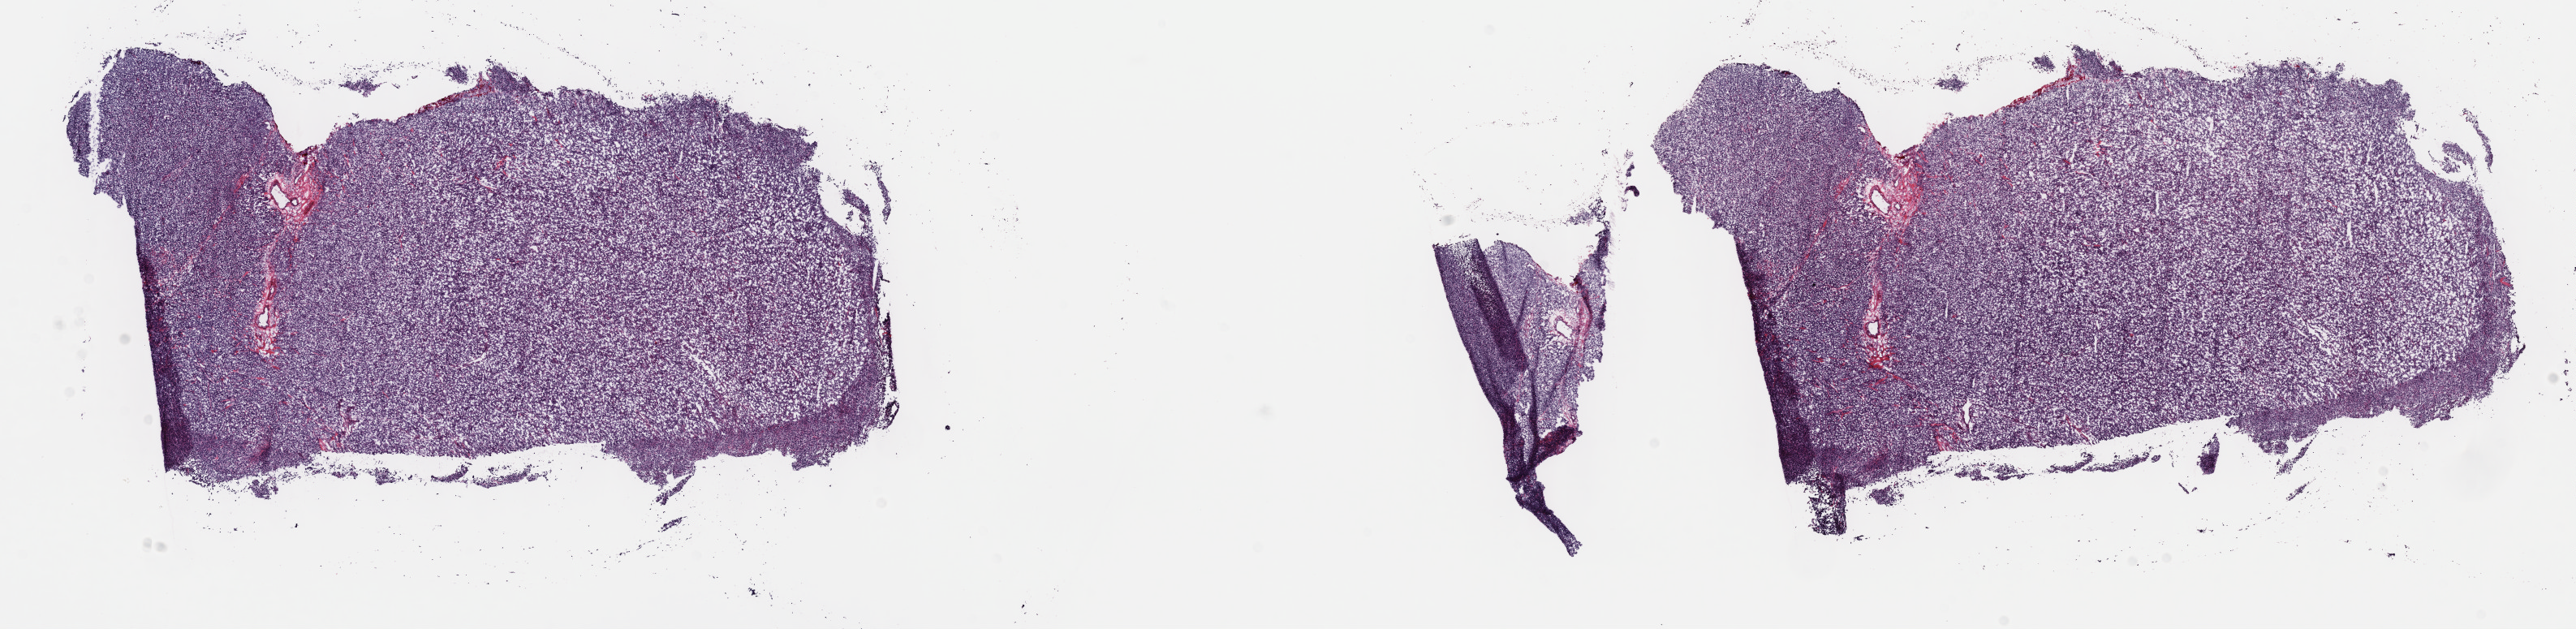
H&E-stained whole-slide image — whole scanned area (about 25.7 x 6.3 mm, slide scanned at 40x) shown as a low-resolution overview. Frozen section from the top of the tissue portion. Primary tumour sample from the bladder. Male, age 60 years at initial diagnosis. Histologic grade: high grade. Slide review estimates, as recorded: tumour cells 90%, tumour nuclei 96%, normal cells 0%, stromal cells 7%, necrosis 3%. Infiltration values recorded for this section: lymphocyte infiltration 2%, monocyte infiltration 0%, neutrophil infiltration 0%.
- AJCC pathologic stage: IV
- lymph nodes positive (case pathology): 1 of 170 examined
- pathologic diagnosis: Transitional cell carcinoma